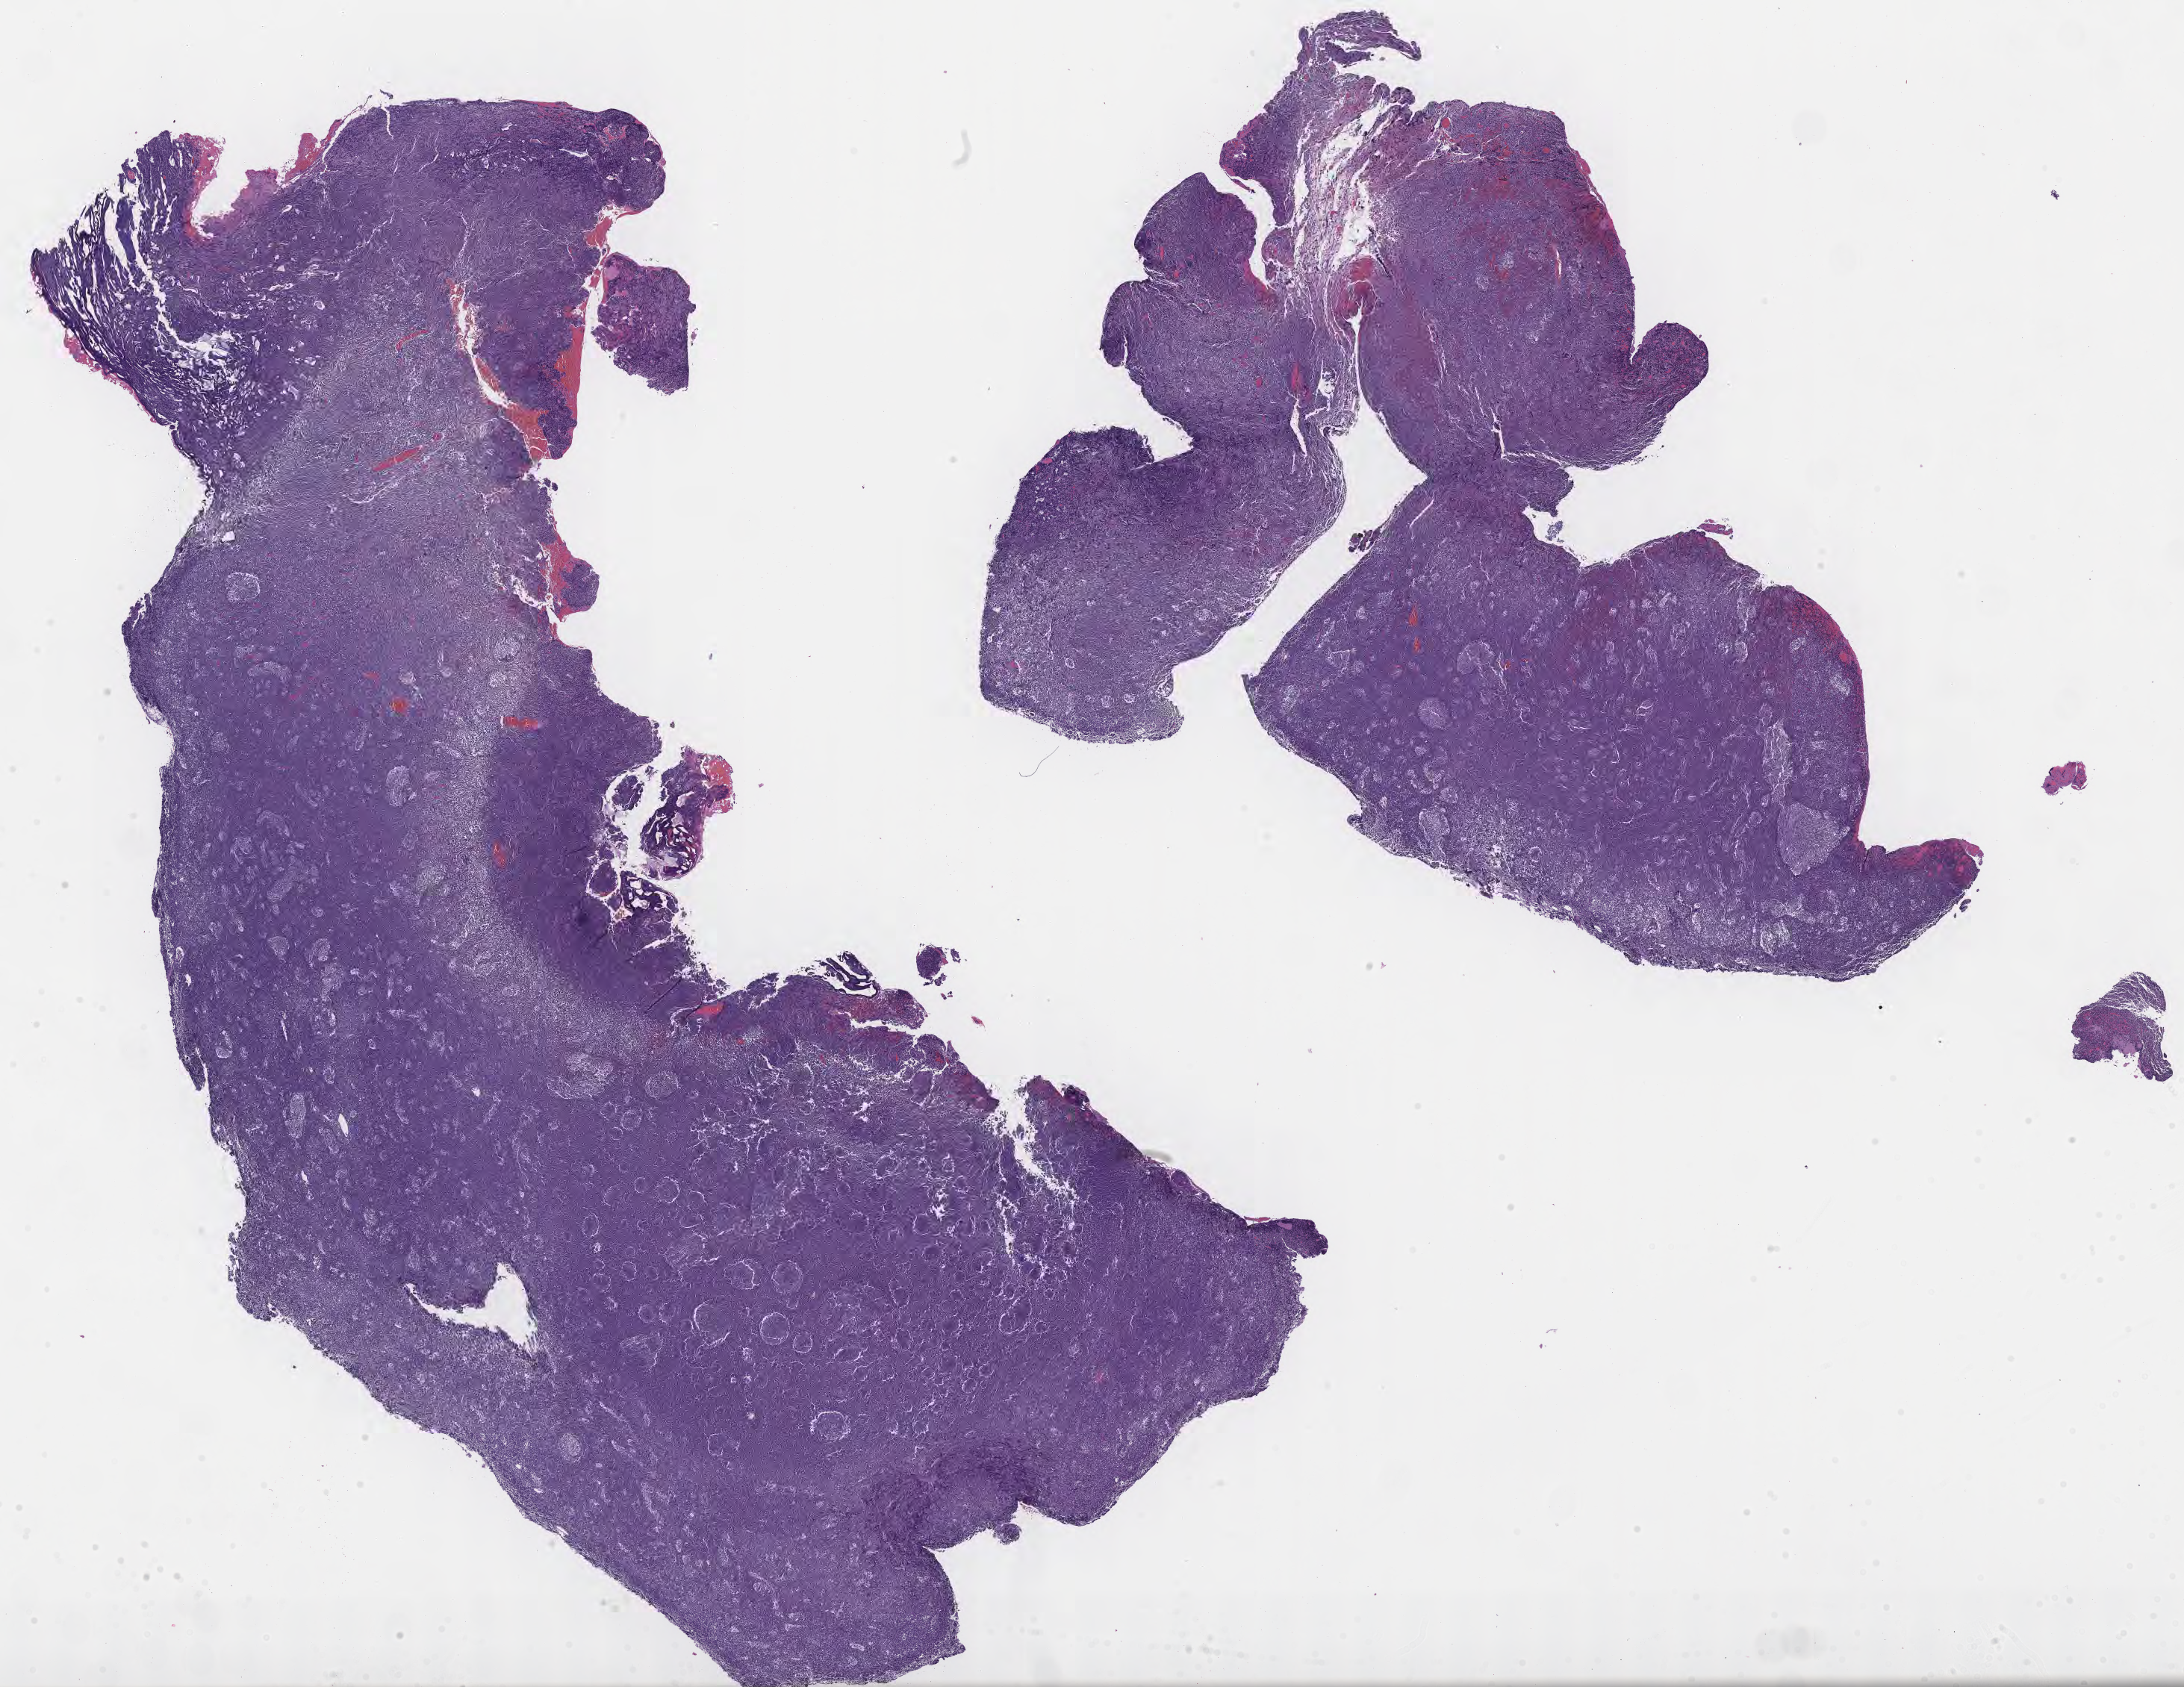
Digitized H&E-stained section of tumor tissue from the brain, whole scanned area (about 23.6 x 18.3 mm) shown as a low-resolution overview; formalin-fixed, paraffin-embedded (FFPE) tissue. Patient: female, age 534 days (about 1.5 years).
Diagnosis (ICD-O-3 morphology term): Medulloblastoma, NOS.